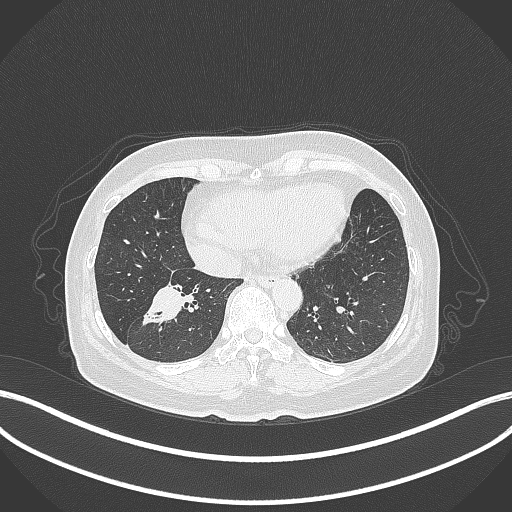
Chest CT, one axial slice; position 125 of 429 along the scan axis; lung window (W 1500 / L -600 HU); 1 mm slice thickness; 512 × 512 image matrix. Female patient, age 67 years. From the clinical record (not read from this slice): clinical TNM (as recorded): T1c N1 M0.
Outlined on this slice (rectangle marked by the reading radiologist):
- lung tumour (recorded histology: adenocarcinoma): bounding box [x1, y1, x2, y2] px = [137, 281, 188, 328]